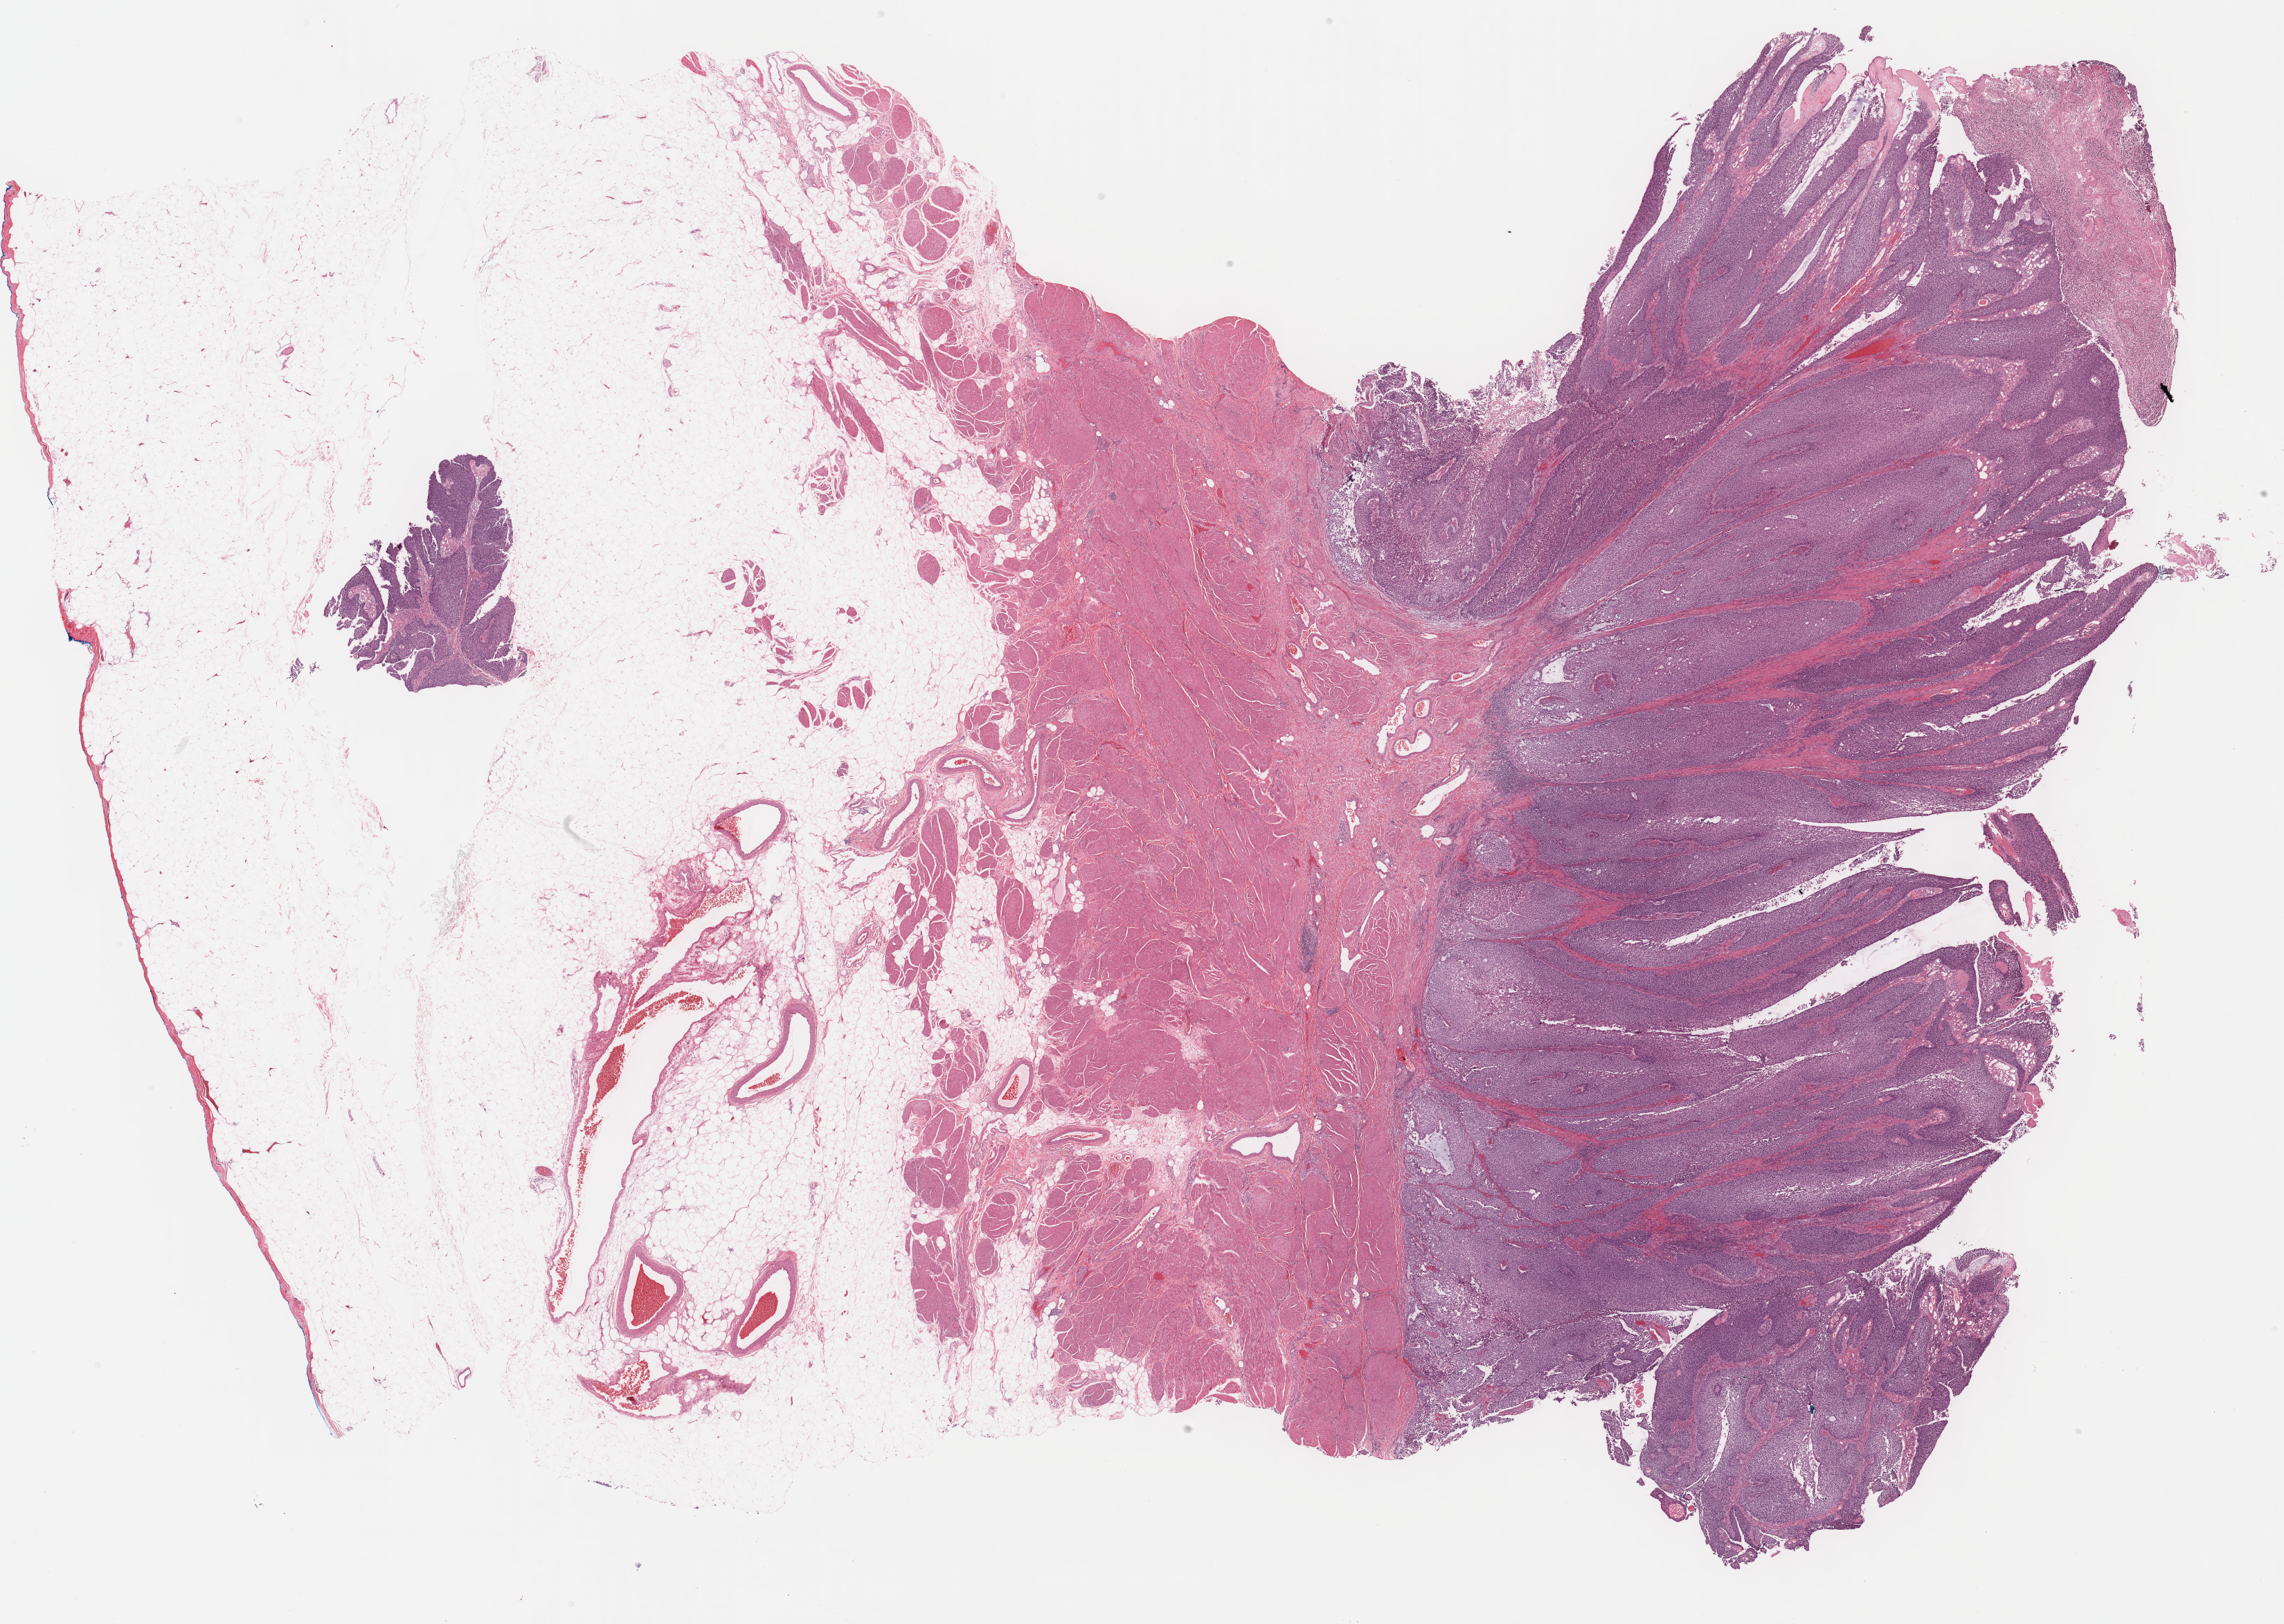
H&E-stained whole-slide image, low-resolution overview of the scanned area, about 26.7 x 19.0 mm (slide scanned at 40x), FFPE section, sample: primary tumour, bladder. Patient: male, age at initial diagnosis 68 years. Histologic grade: high grade.
Histologic diagnosis: Transitional cell carcinoma. AJCC pathologic stage: II.